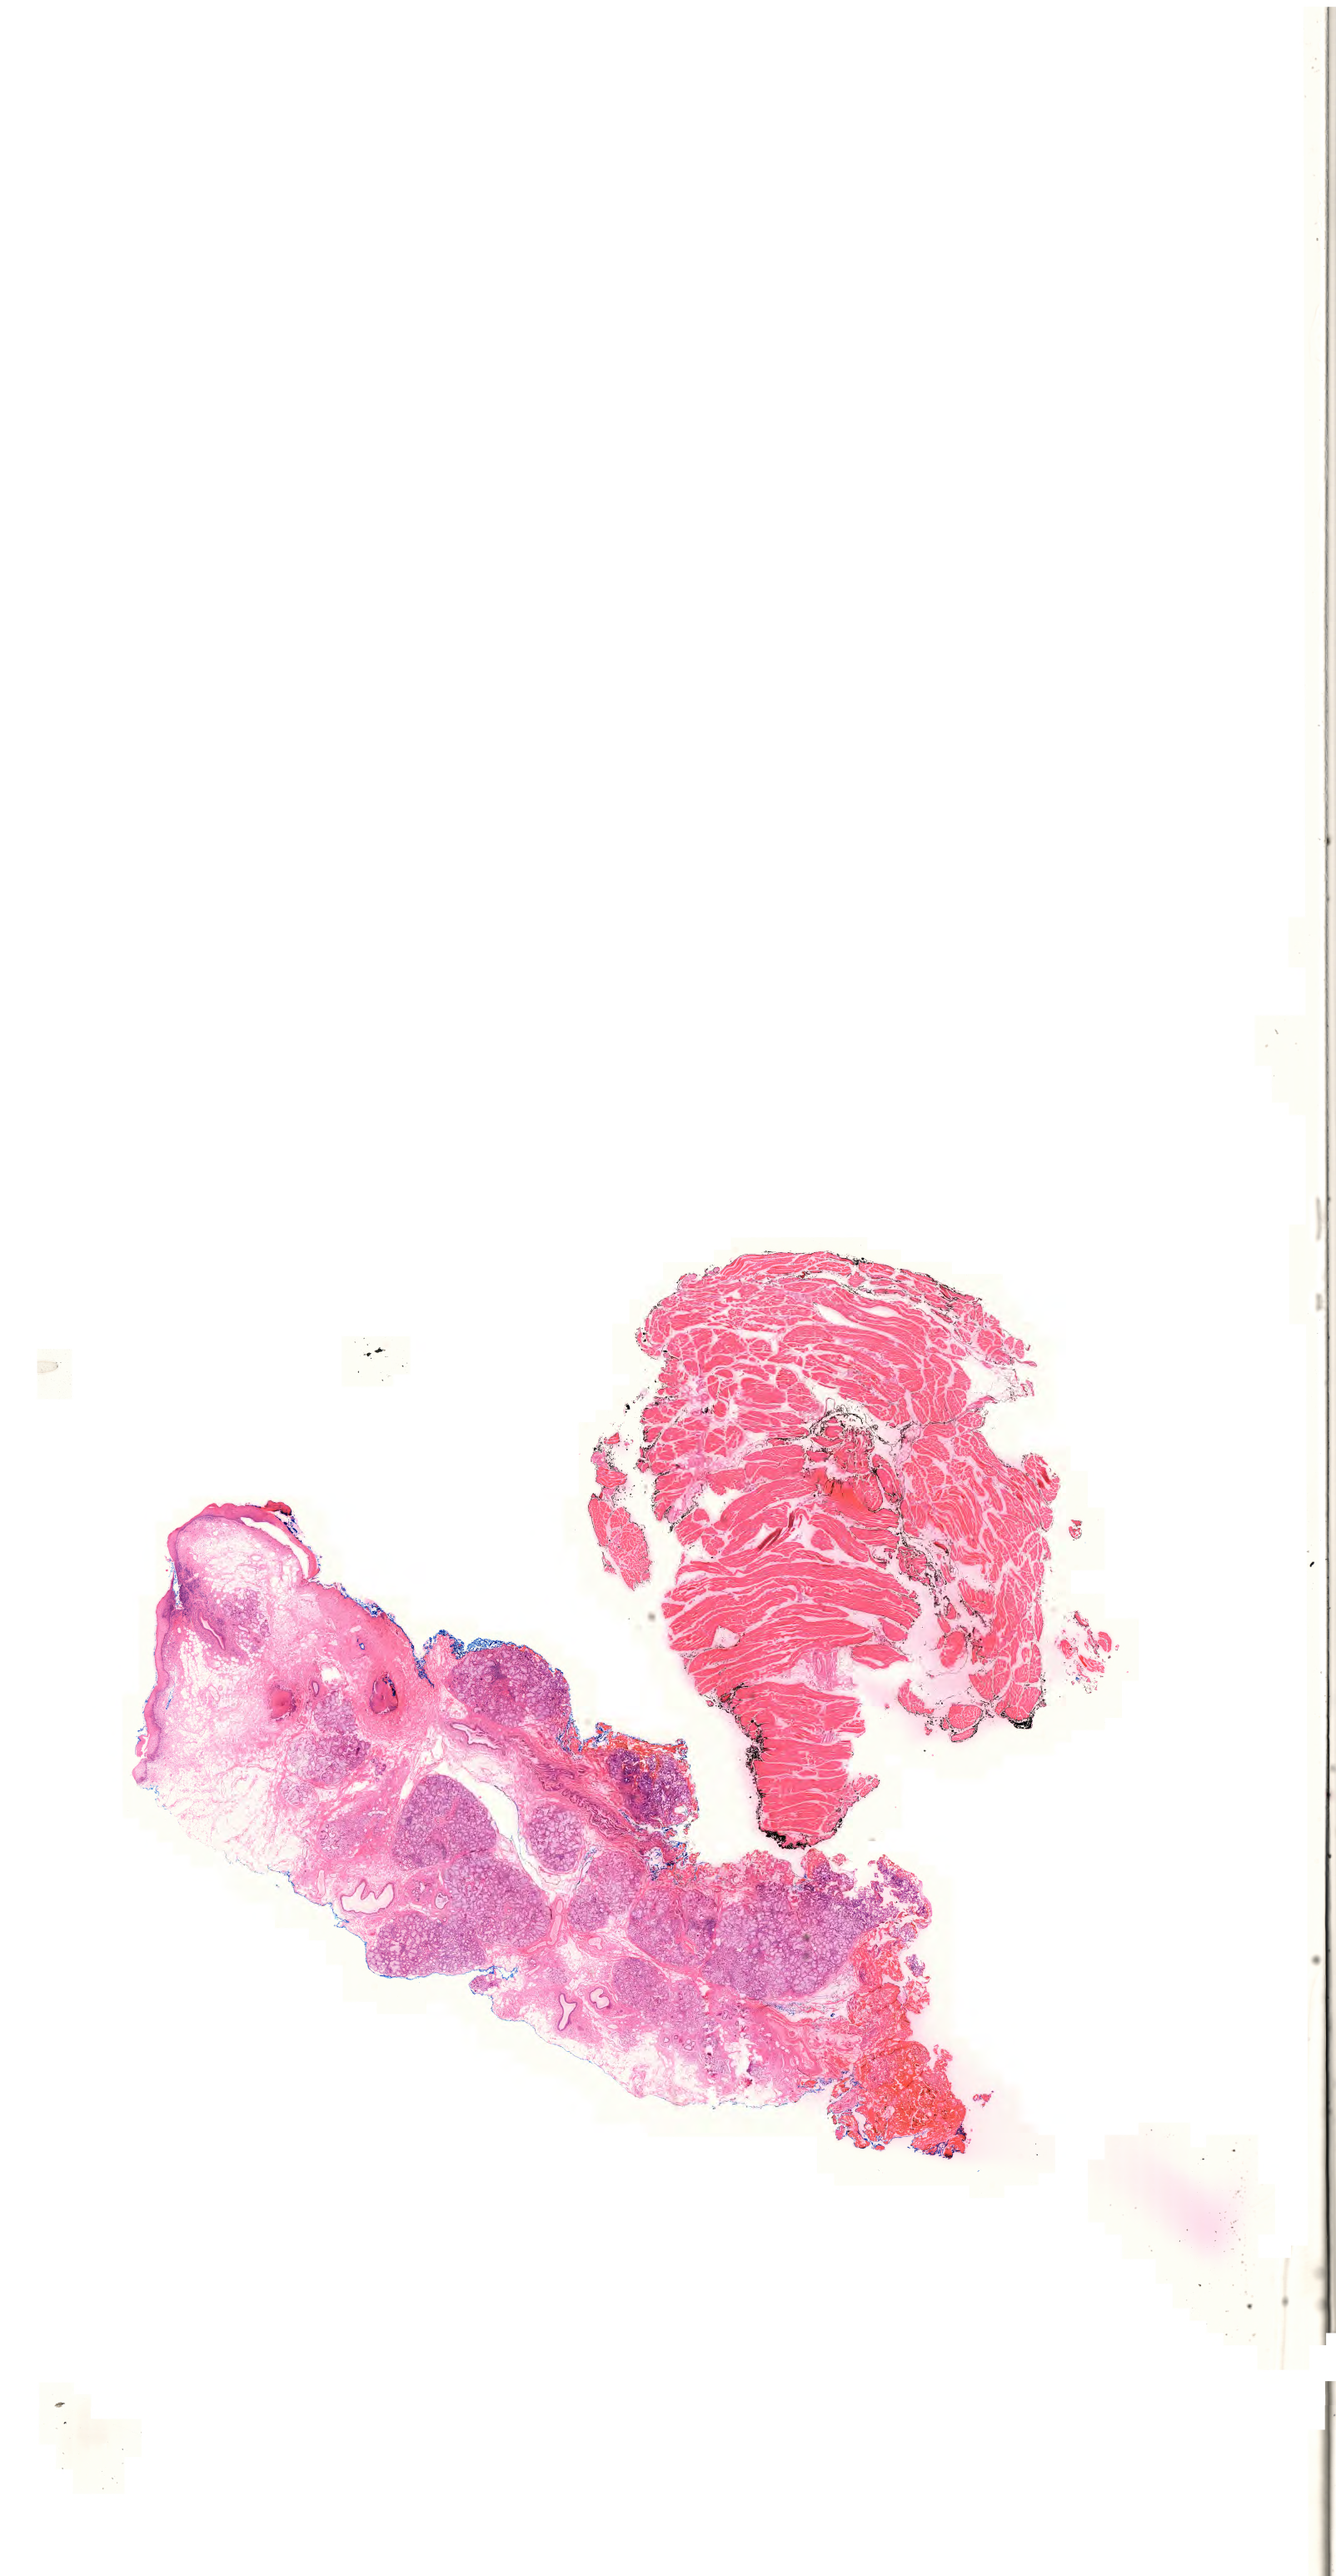
Whole-slide histology image, Hematoxylin and eosin (H&E) stained, a low-resolution overview of the entire scanned area, about 23.9 x 46.0 mm (from a 20x scan), formalin-fixed paraffin-embedded (FFPE) diagnostic section, primary tumour sample from the head and neck. Male, age 79 years at initial diagnosis. Histologic grade: G3 (poorly differentiated).
* TNM: T2 N2c MX
* laterality: midline
* AJCC pathologic stage: IVA (7th edition)
* histologic diagnosis: Squamous cell carcinoma, NOS (floor of mouth, NOS)